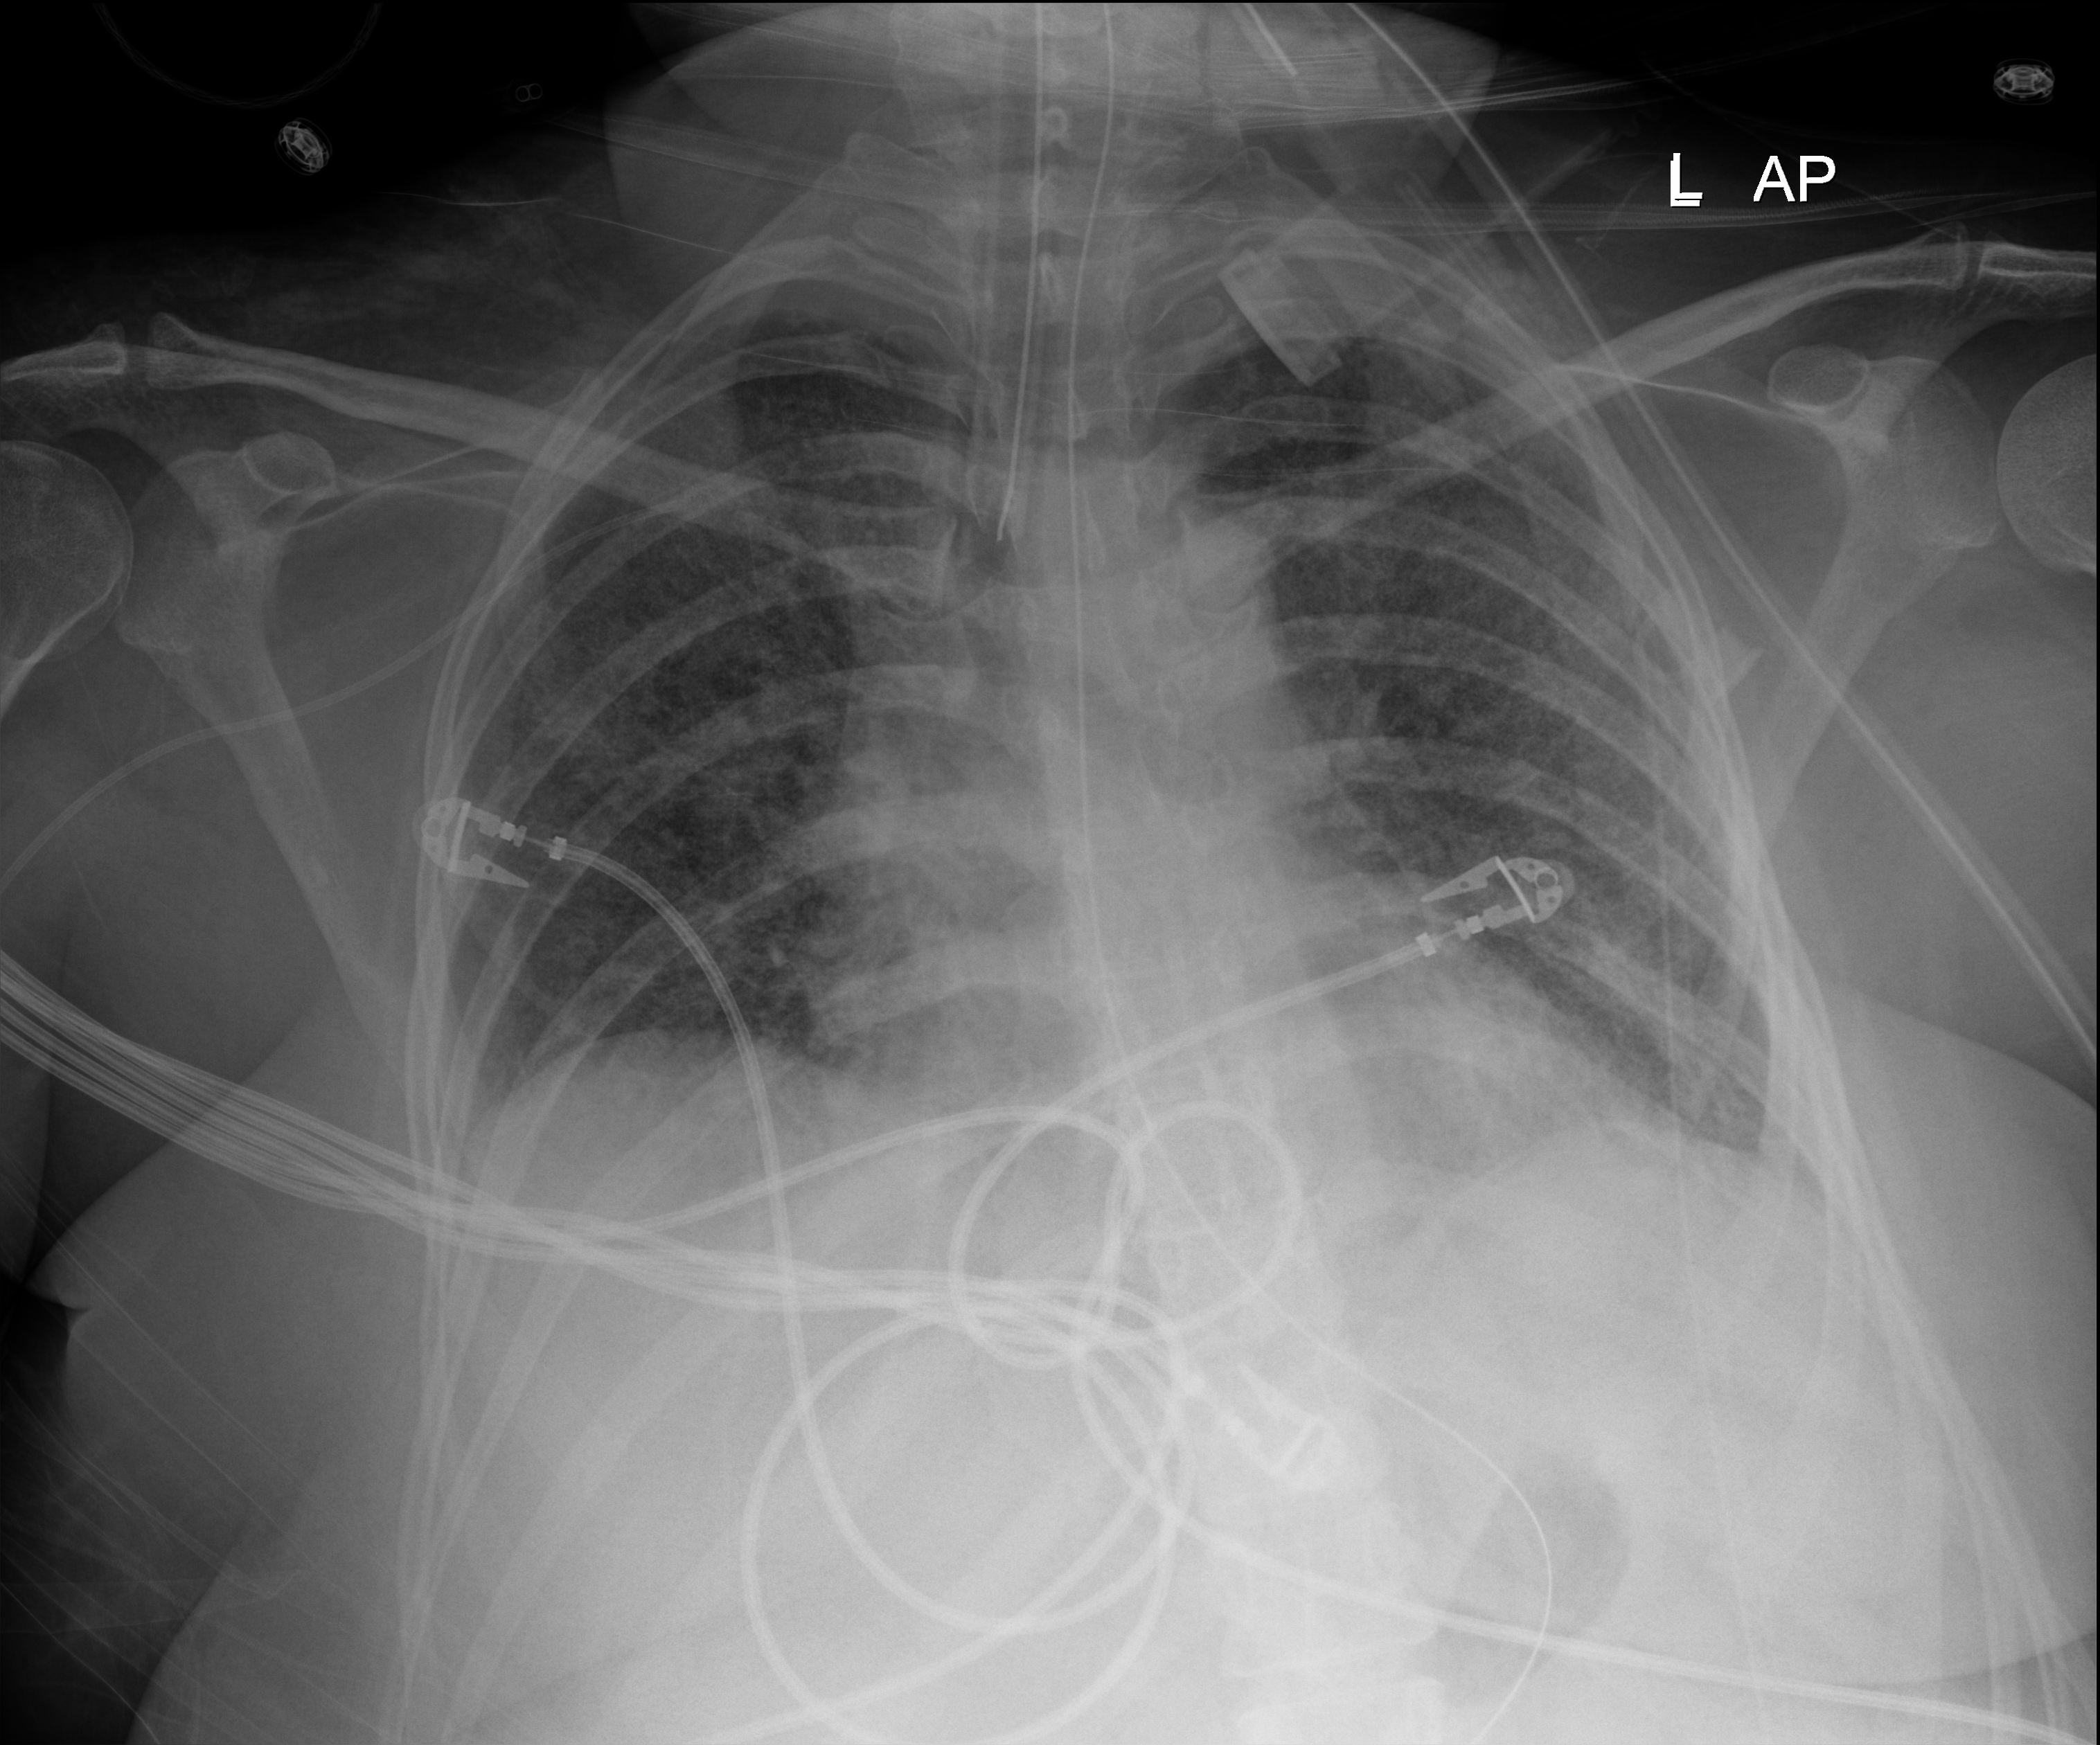
Chest X-ray (portable); anteroposterior (AP) projection. Female patient hospitalised with COVID-19, age 18–59 years.
Hospital-stay facts (about this admission, not read from this image; timing relative to this image not recorded): admitted to intensive care during this hospital stay: yes.